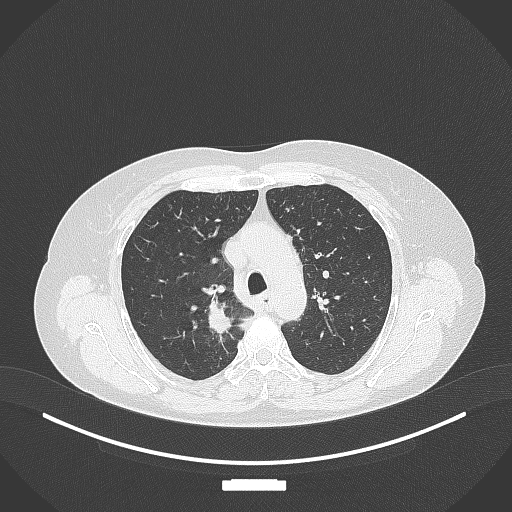
Chest CT, one axial slice. 120 kVp. Lung window (W 1500 / L -600 HU). 1 mm slice thickness. 512 × 512 image matrix. Patient: female, 62 years. From the clinical record (not read from this slice): clinical TNM (as recorded): T1c N1 M0.
Structures marked on this image (rectangle marked by the reading radiologist):
- lung tumour (recorded histology: squamous cell carcinoma): box from (x=207, y=297) to (x=236, y=334) px